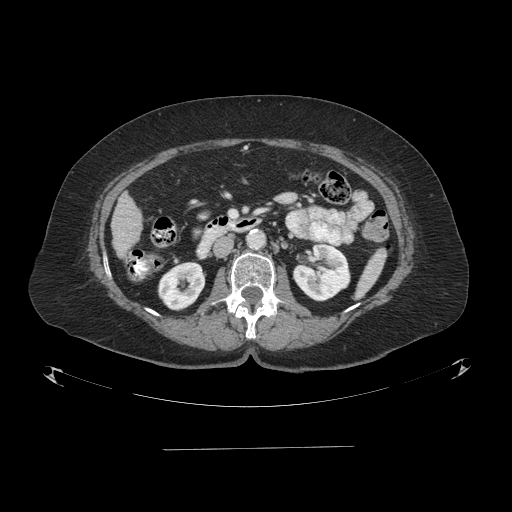
Contrast-enhanced abdominal CT (liver protocol), one axial slice. Position 23 of 103 along the scan axis. One of 2 acquisitions stored at this slice position. Soft-tissue window (W 400 / L 40 HU). 2.5 mm slice thickness. 512 × 512 image matrix. From the clinical record (not read from this slice): diagnosis: hepatocellular carcinoma (patient treated with transarterial chemoembolisation; whether this scan precedes or follows treatment is not stated here); TNM stage (as recorded): Stage-IIIA; Child-Pugh class: A; tumour differentiation: poorly differentiated; tumour nodularity: multinodular.
Structures marked on this image (semi-automatically segmented with operator editing):
- liver parenchyma outside the tumour (the mass and vessels are separate outlines, so this box may not span the whole liver): bounding box [x1, y1, x2, y2] px = [110, 192, 142, 262]